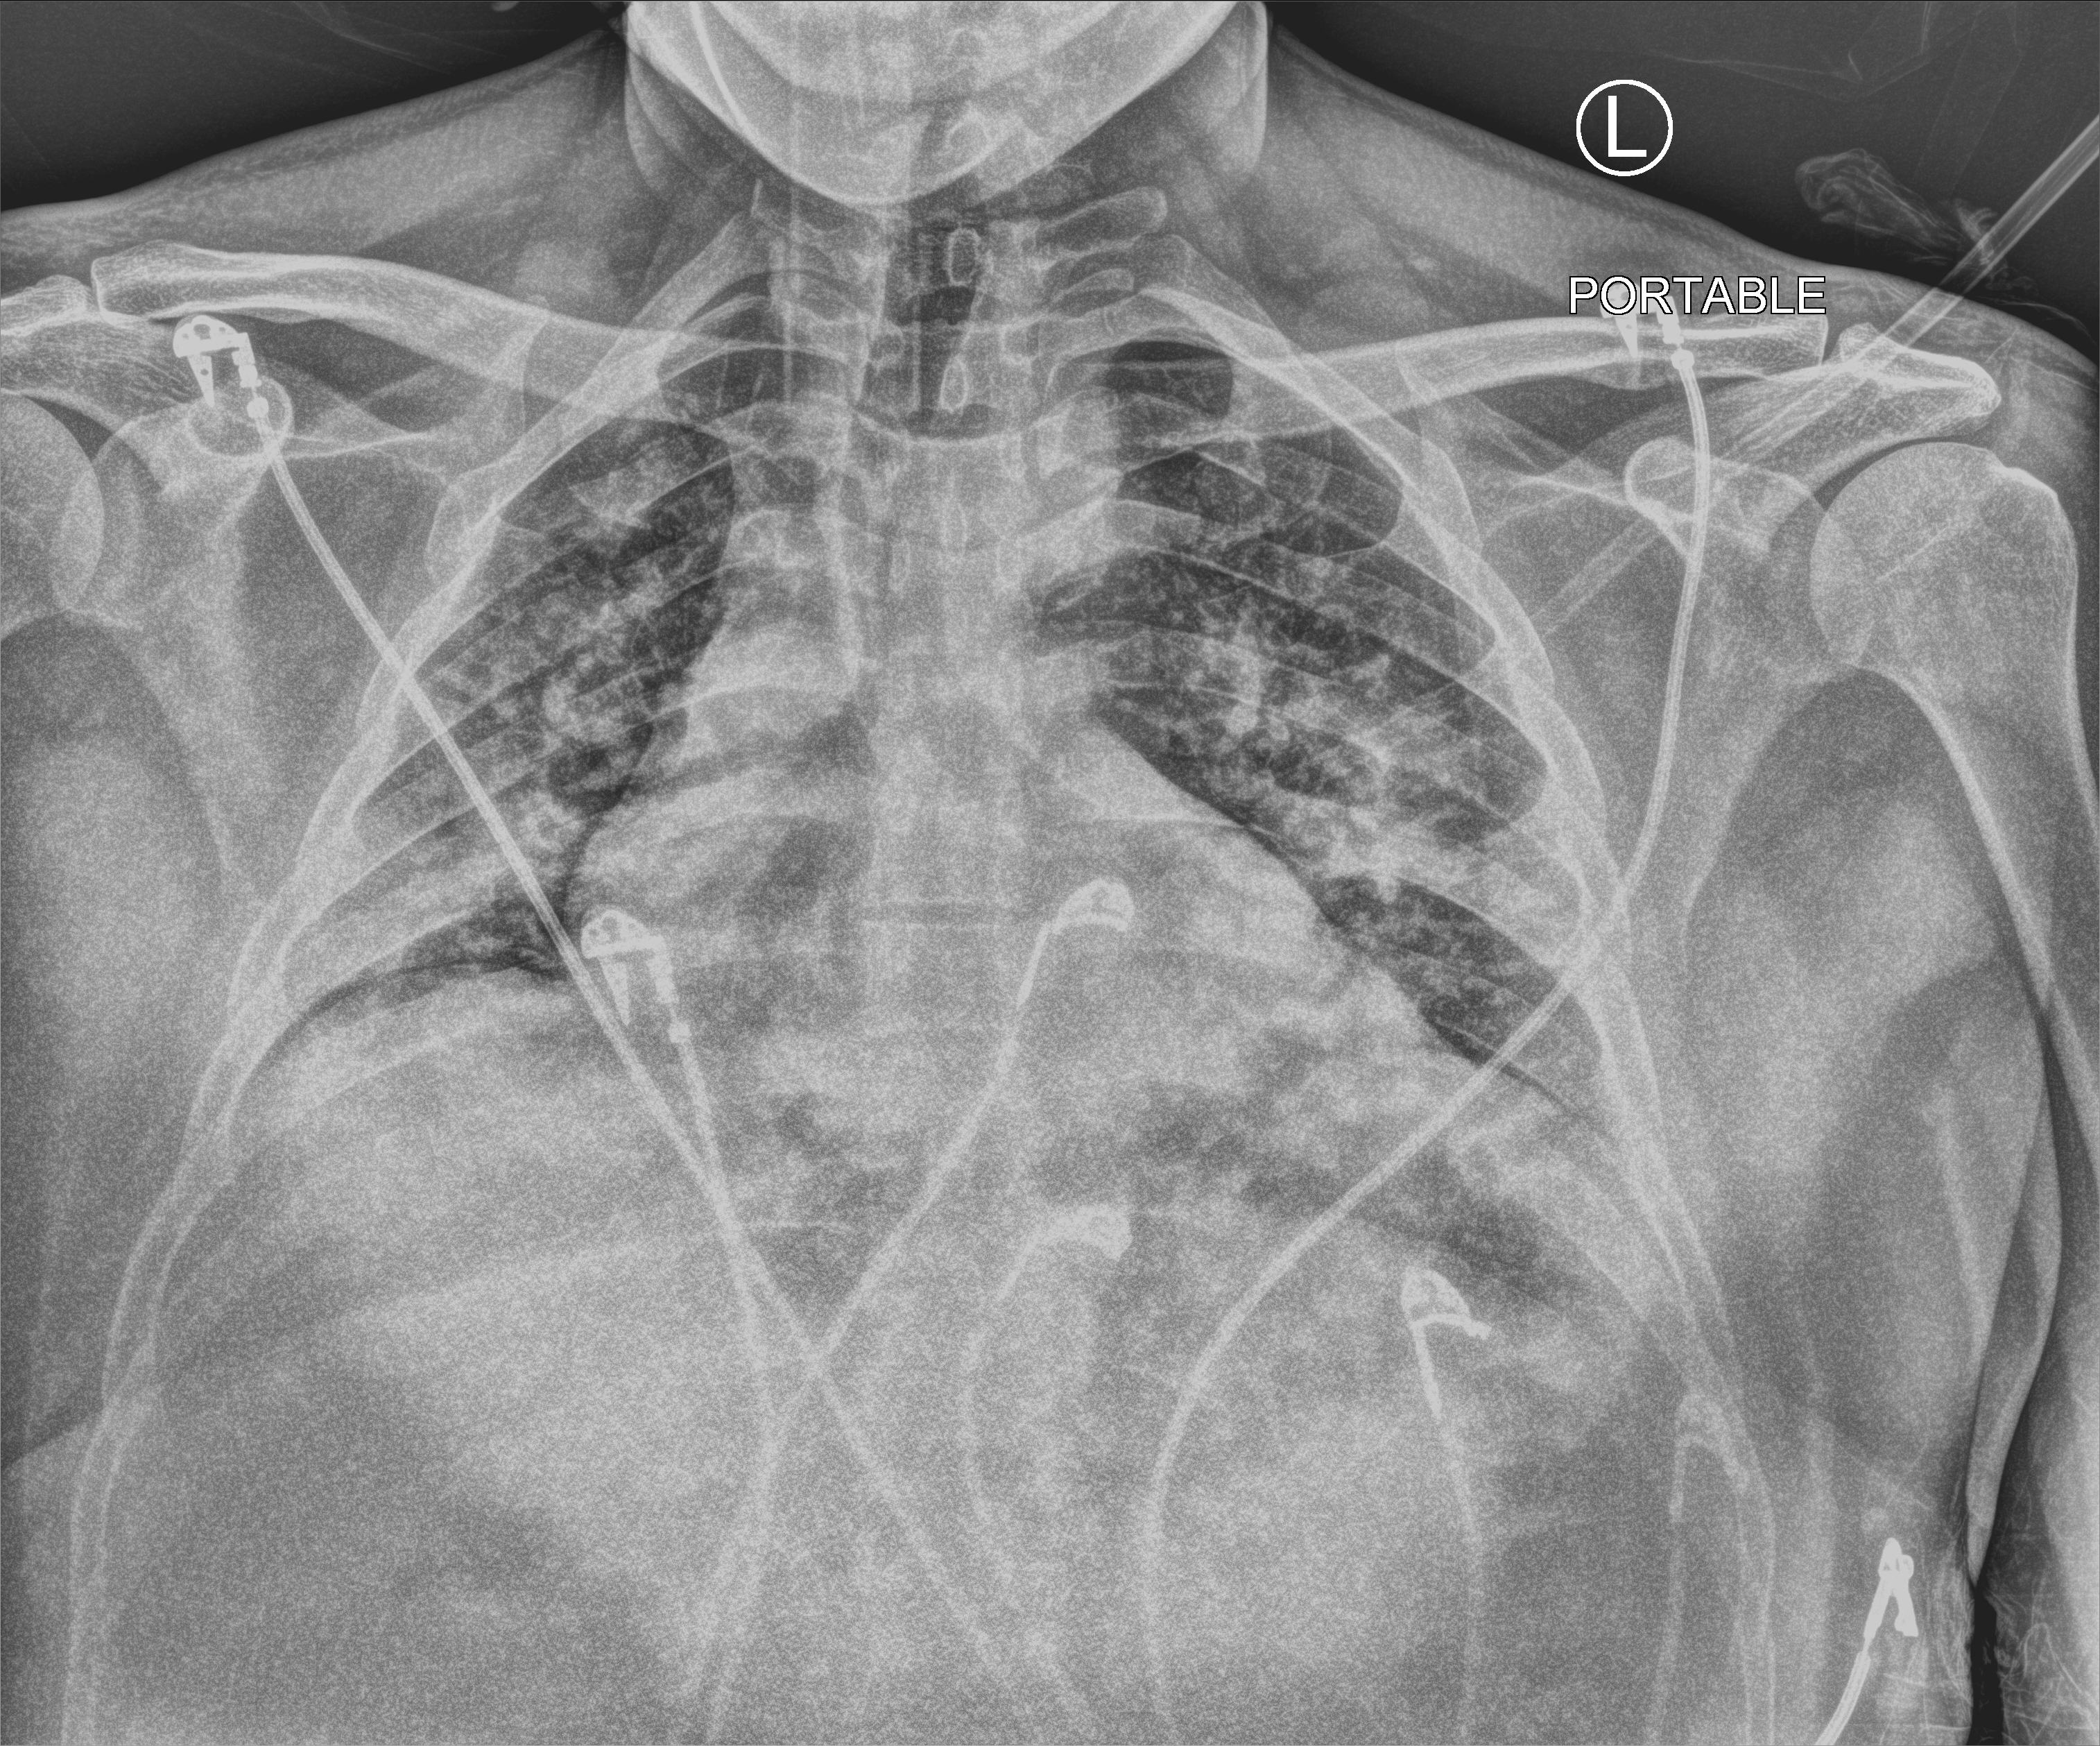
Bedside chest radiograph (computed radiography). Patient hospitalised with COVID-19; male, aged 18–59 years.
Hospital-stay facts (about this admission, not read from this image; timing relative to this image not recorded):
- admitted to intensive care during this hospital stay: no